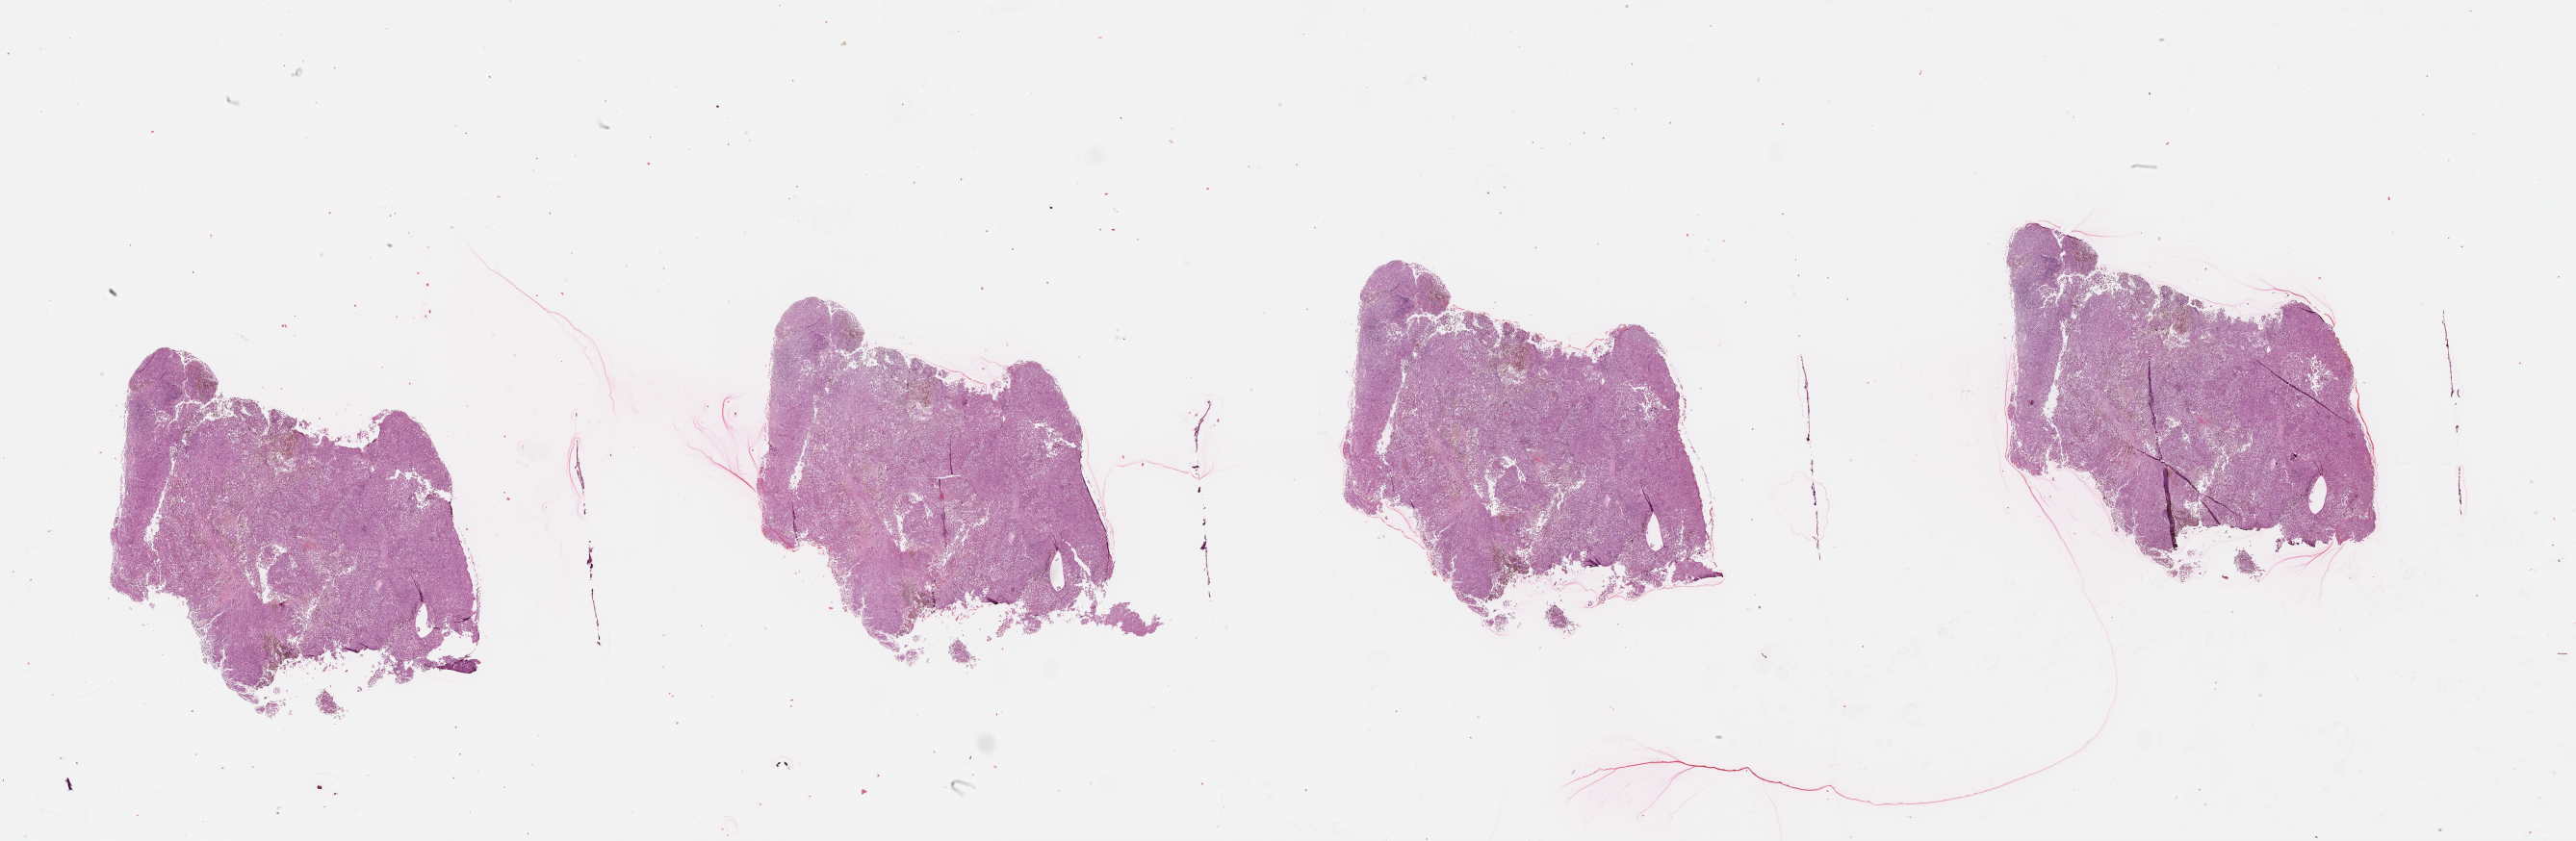
Whole-slide histology image, Hematoxylin and eosin (H&E) stained, shown as a low-resolution overview of the whole scanned area (about 43.1 x 14.1 mm). Male, 87 y/o.
Patient diagnosis: Malignant melanoma, NOS.